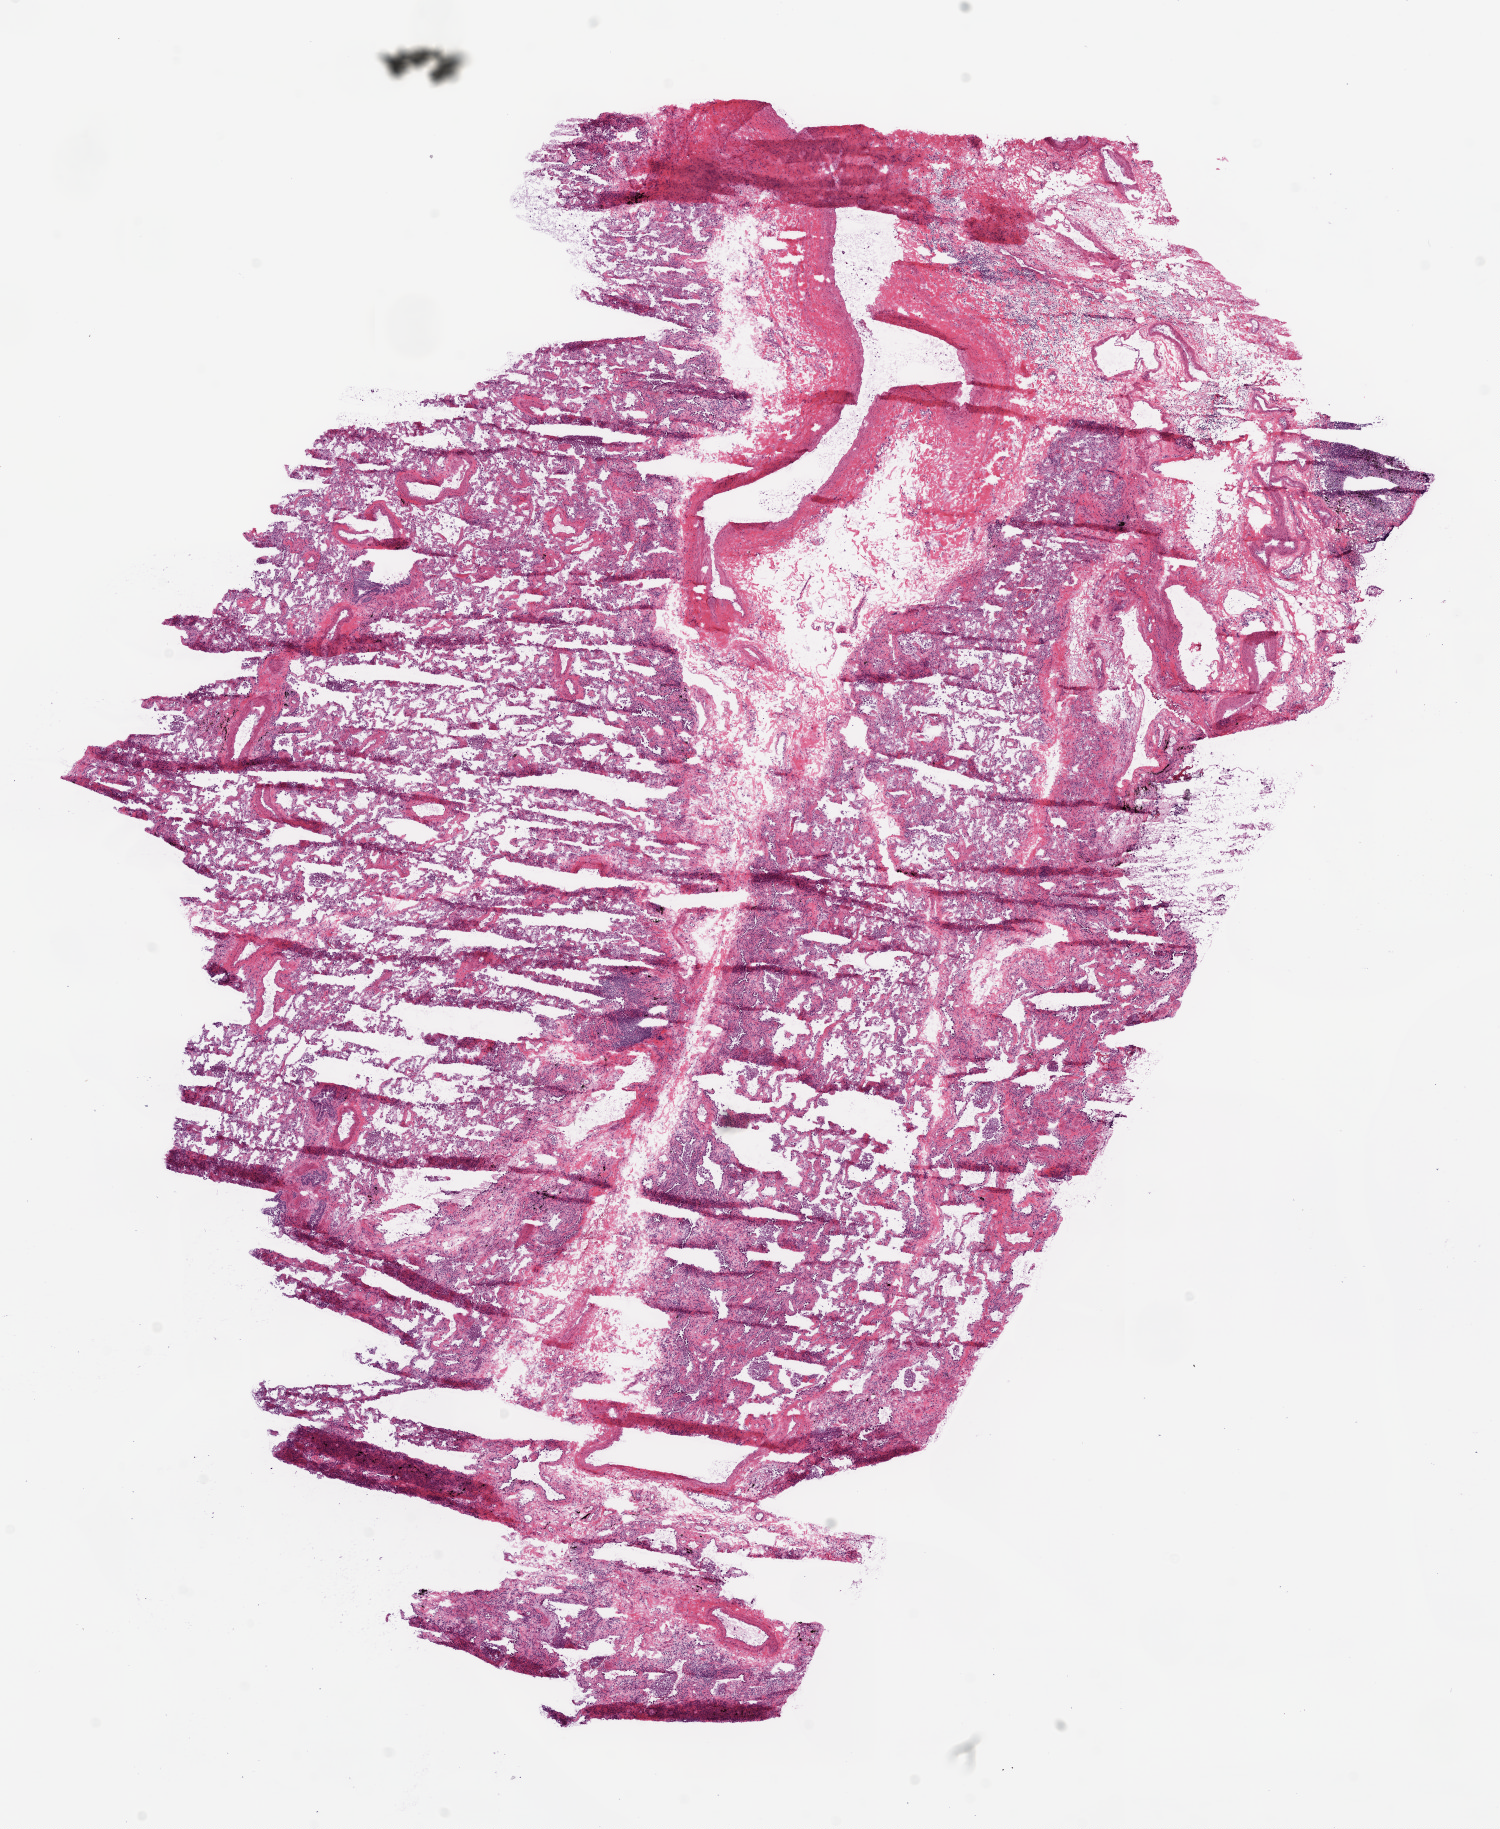
Digitized H&E tissue section (whole slide), a low-resolution overview of the entire scanned area, about 12.0 x 14.7 mm (acquisition: 20x scan). Frozen section from the bottom of the tissue portion. Sample: solid tissue normal (non-tumour tissue), lung. Patient: female, age at initial diagnosis 60 years.
• this section: solid tissue normal (non-tumour) sample from the same patient
• patient diagnosis: Adenocarcinoma, NOS